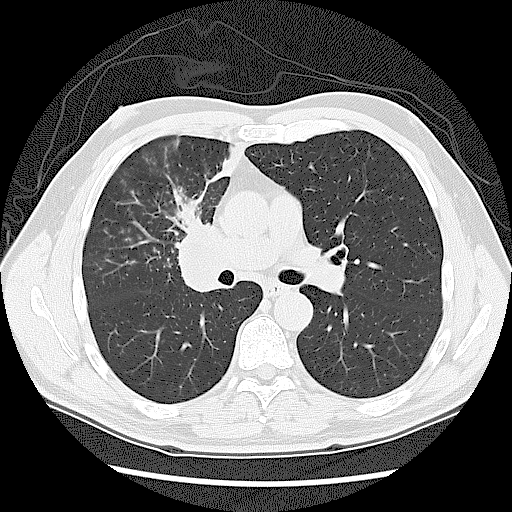
Low-dose screening chest CT, axial slice, first (baseline) screen, lung window (W 1500 / L -600 HU), lung (sharp) reconstruction kernel (LUNG), 120 kVp, slice 58 of 131 in the series. Male participant, aged 60 years at enrolment. Current smoker at enrolment.
Lesion marked by an expert reader, bounding box <158,217,241,308> (left, top, right, bottom; pixels). Screening reader's record for this exam: no non-calcified nodule ≥4 mm recorded. Participant outcome: lung cancer diagnosed 41 days after this screen — small cell carcinoma, NOS, right upper lobe, stage IIIA (AJCC 6th edition).